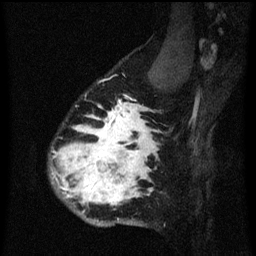
Breast MRI (dynamic contrast-enhanced), one sagittal slice; slice 49 of 60 in the series (ordered by position); dynamic contrast-enhanced series, image 2 of 3 at this slice position (ordered by acquisition); 1.5 T; TE 4.2 ms, TR 8.4 ms; 2 mm slice thickness; 256 × 256 image matrix, field of view 180 × 180 mm. Female patient, age 34 years. From the clinical record (not read from this slice): setting: breast cancer imaged before/during neoadjuvant chemotherapy; receptor status: HR-positive, HER2-negative.
Annotated regions visible in this slice (semi-automatic segmentation, software-assisted and operator-edited):
- analysis volume of interest (the breast-tissue region the enhancement analysis was run in; not a lesion): bounding box [x1, y1, x2, y2] px = [50, 58, 173, 229]
- tumour enhancement mask (voxels above the 70 % enhancement threshold inside the analysis volume of interest): [52, 104, 157, 207]